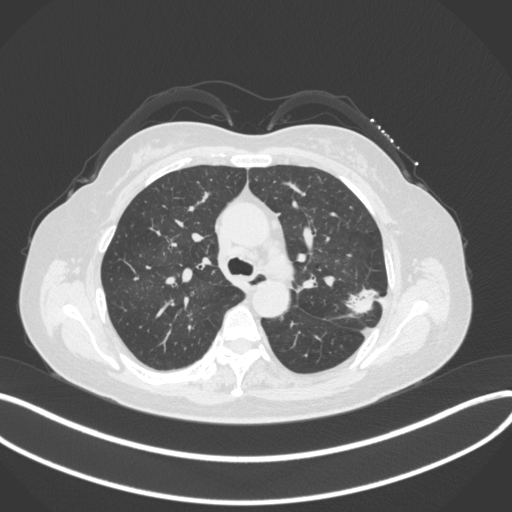
Chest CT, one axial slice; position 229 of 330 along the scan axis; lung window (W 1500 / L -600 HU); 1 mm slice thickness; 512 × 512 image matrix, field of view 400 × 400 mm. Female patient, age 60 years. Case-level facts recorded for this patient, not image findings: clinical TNM (as recorded): T1c N0 M0.
Outlined on this slice (bounding box drawn by a radiologist):
- lung tumour (recorded histology: adenocarcinoma): box from (x=345, y=280) to (x=383, y=318) px